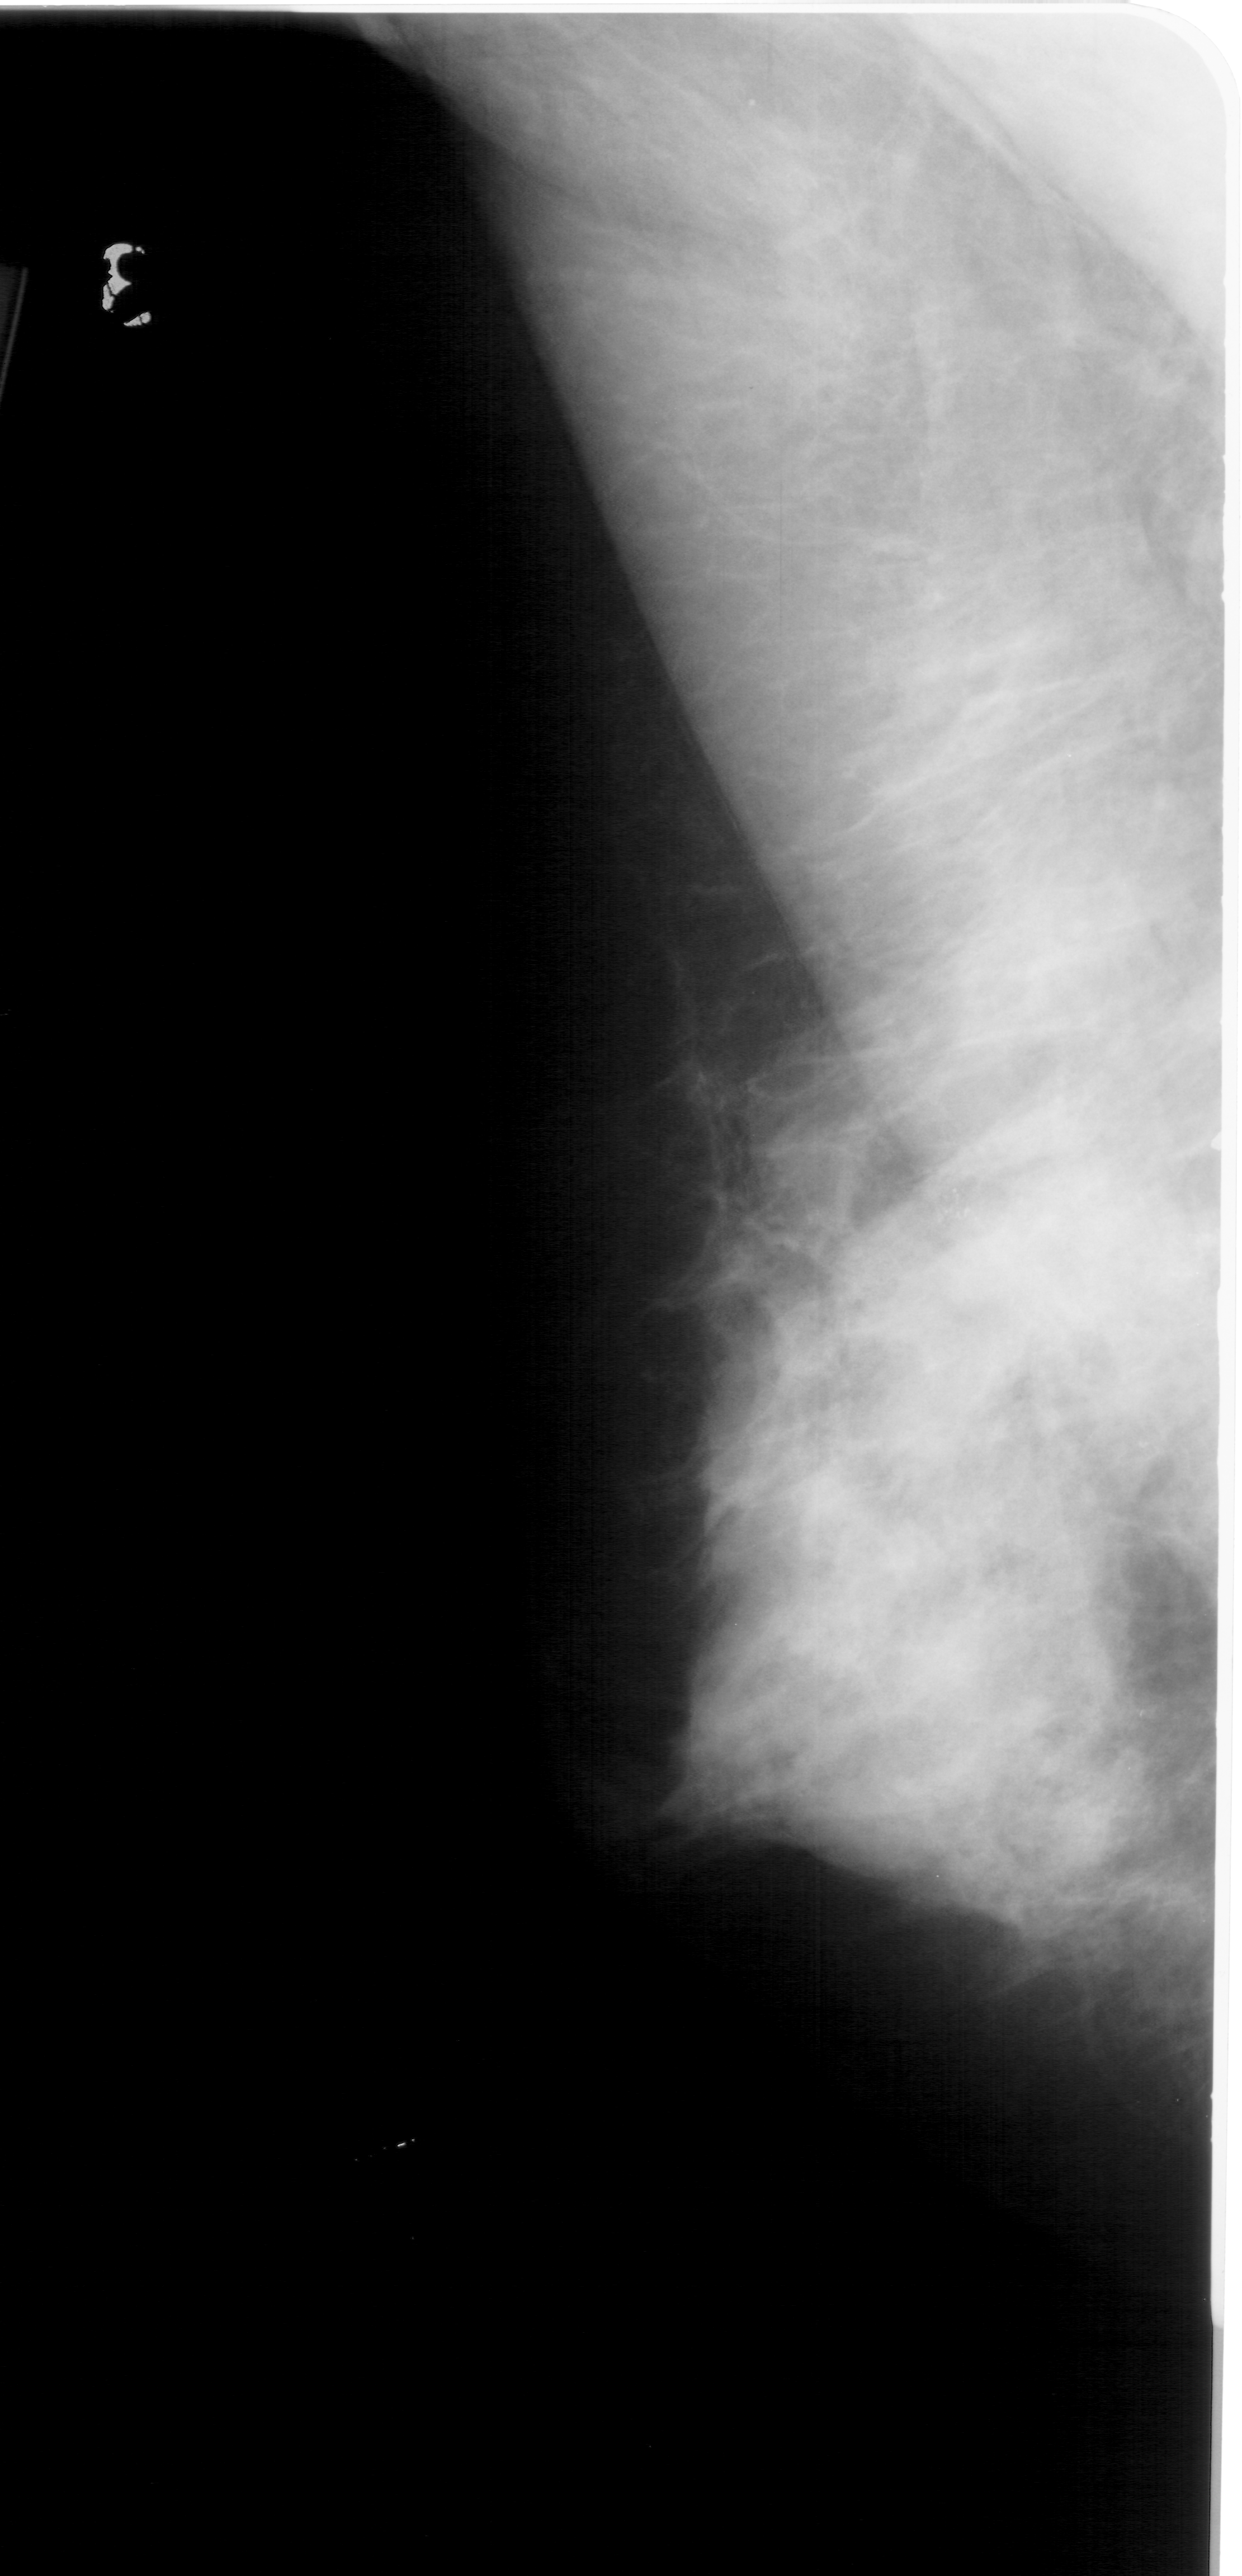
Mammogram (digitized film), left breast, mediolateral oblique (MLO) view, breast composition: extremely dense (BI-RADS density category 4 of 4).
- Marked abnormality: mass, shape irregular, margins ill defined; BI-RADS assessment category 4; pathology result (as recorded, not read from the image): malignant.